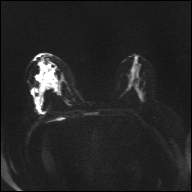
Breast MRI, one axial slice; slice 16 of 32 in the series (ordered by position); diffusion-weighted series; image 2 of 4 stored at this slice position (different b-values; order by instance number); 1.5 T; 4 mm slice thickness; 192 × 192 image matrix. Female patient.
Annotated regions visible in this slice (outlined manually by an expert reader):
- tumour on diffusion-weighted imaging: bounding box (x1, y1, x2, y2) in pixels: (40, 72, 44, 76)